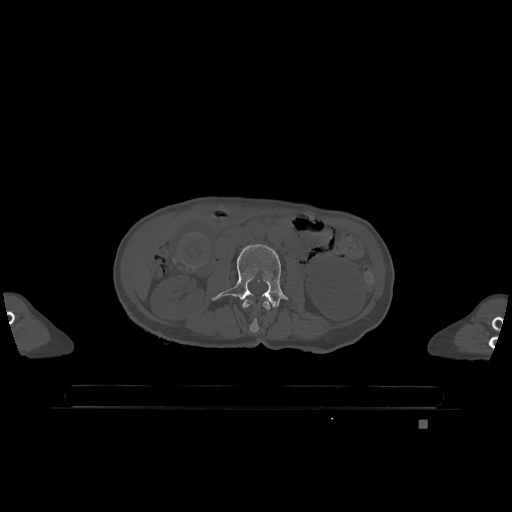
CT including the spine, one axial slice; bone window (W 1800 / L 400 HU); 512 × 512 image matrix, field of view 500 × 500 mm. Patient: female, 74 years. From the clinical record (not read from this slice): primary cancer: lung; vertebrae with lytic lesions (as recorded): T1, T4, T5, T6, L4, L5.
Outlined on this slice (semi-automatic segmentation, software-assisted and operator-edited):
- L2 vertebra: bounding box (x1, y1, x2, y2) in pixels: (242, 299, 270, 333)
- L3 vertebra: (212, 244, 287, 308)